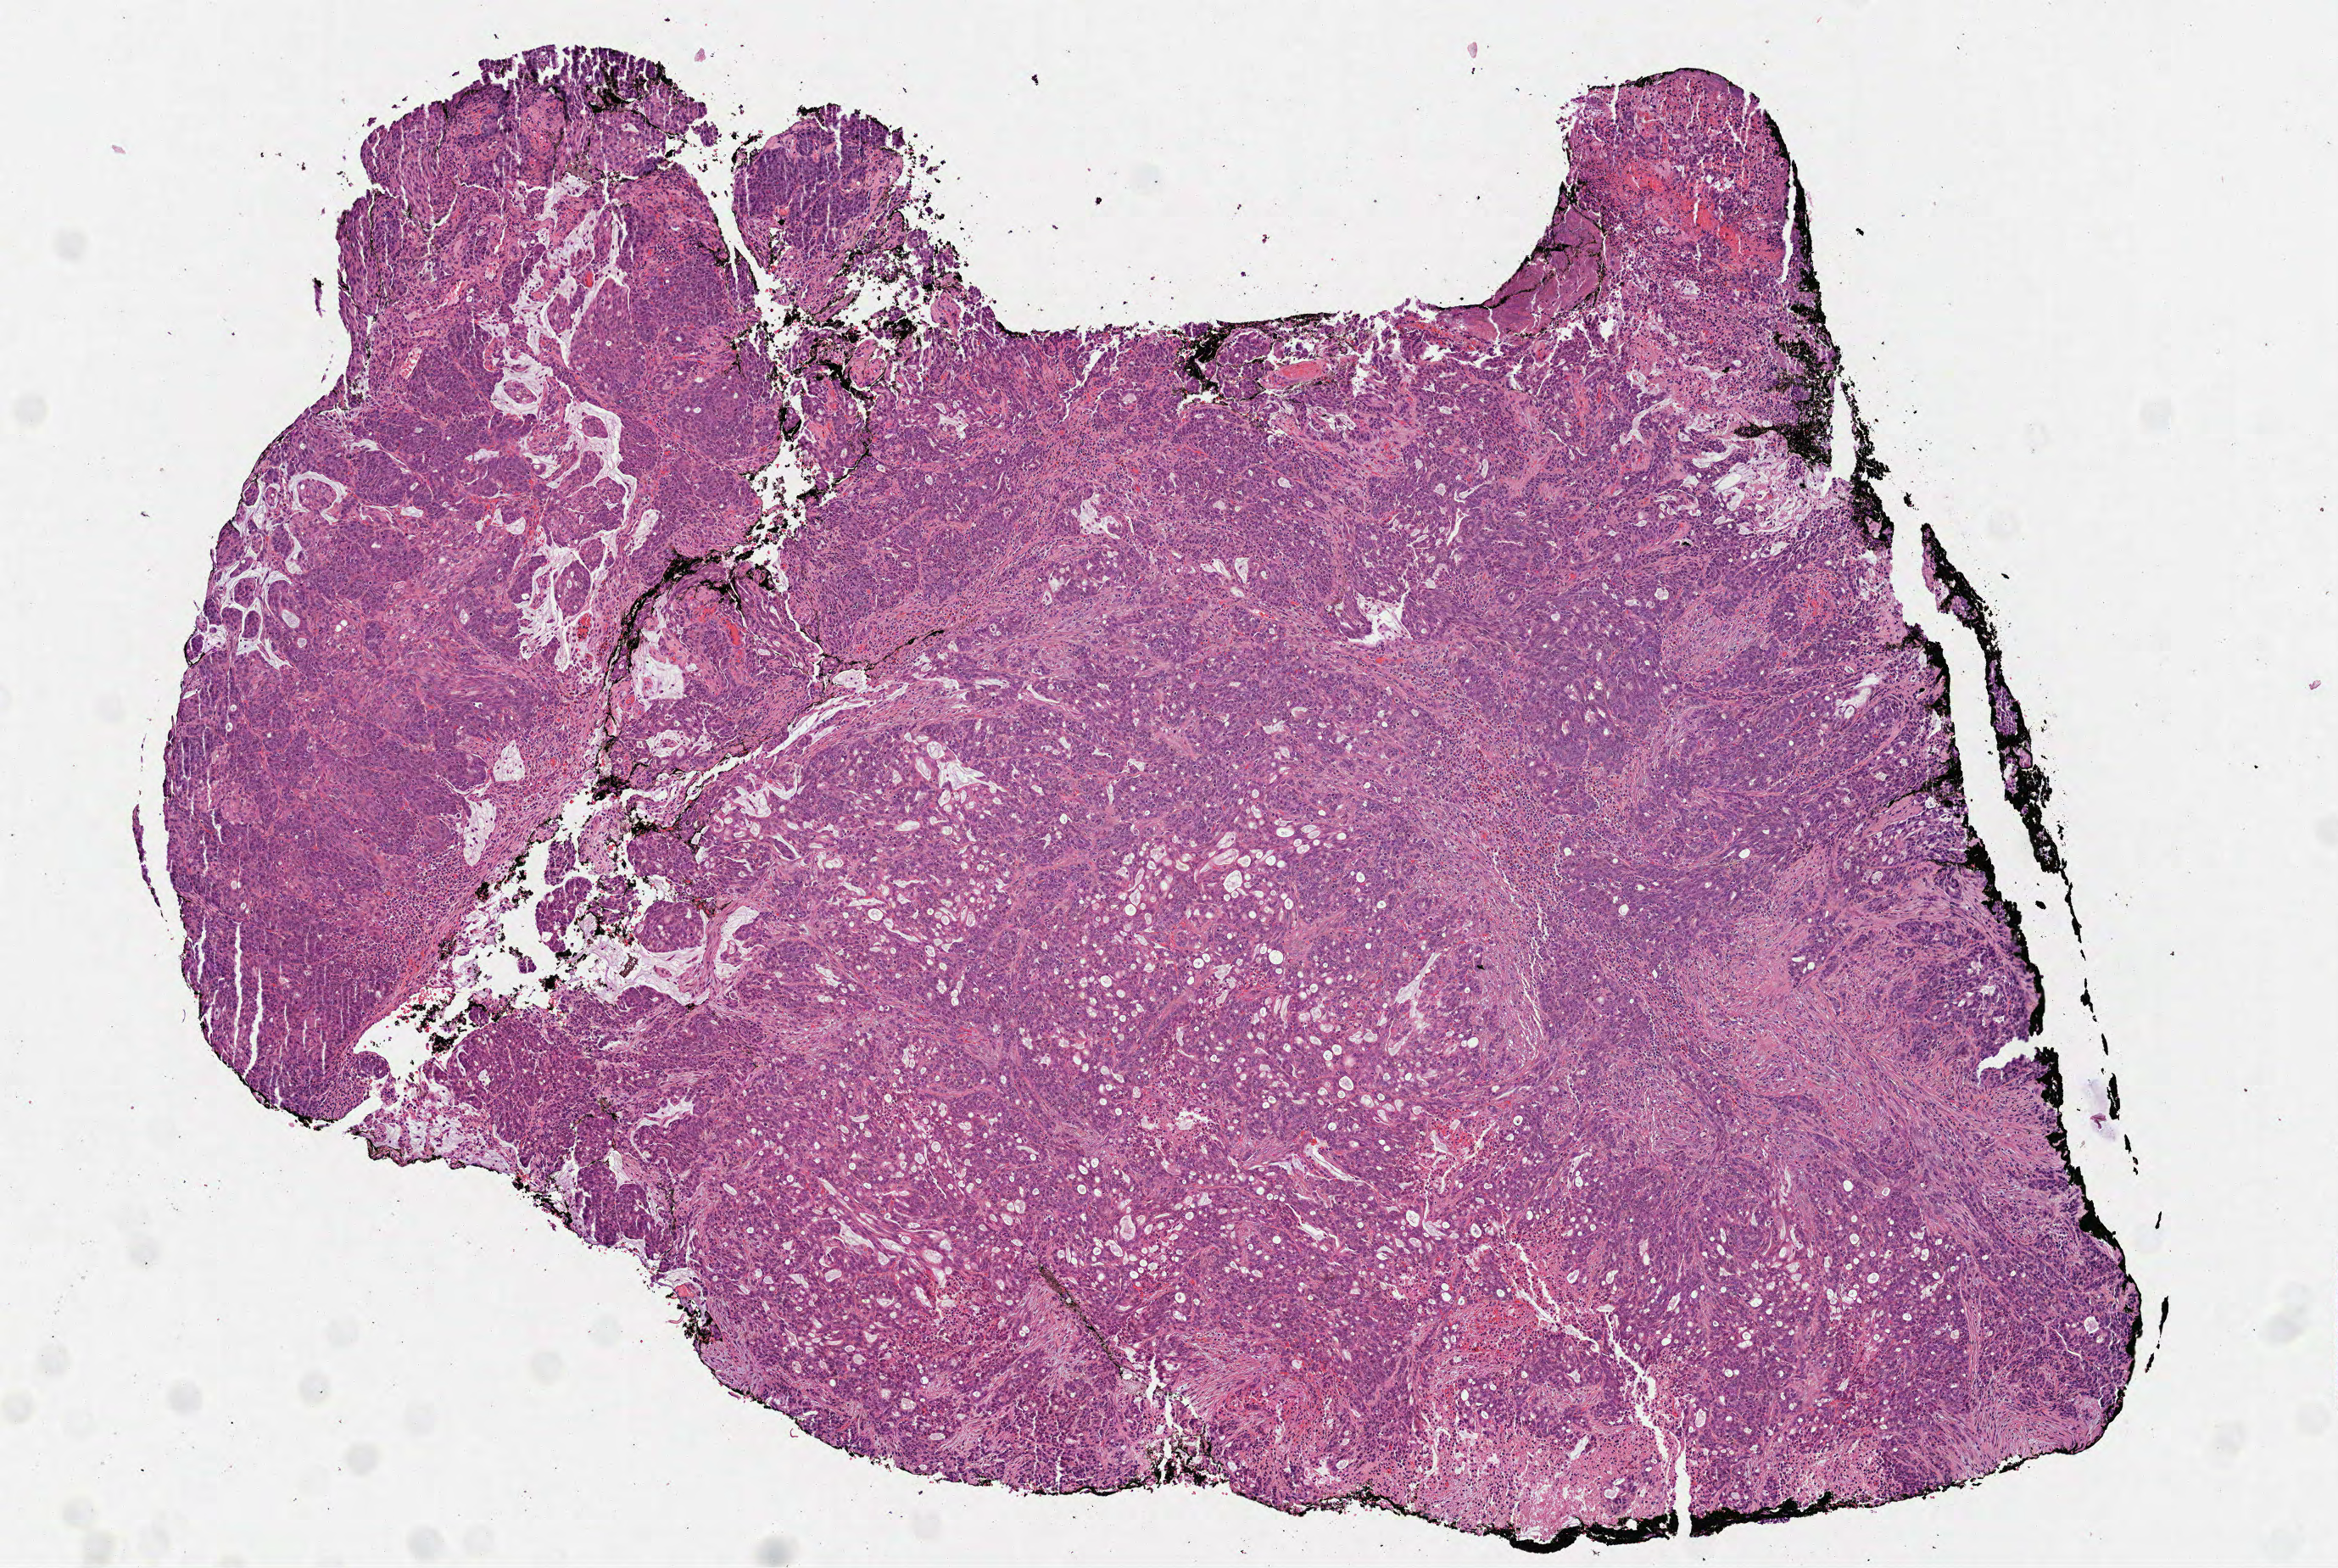
Digitized H&E-stained tissue section (whole slide), shown as a low-resolution overview of the whole scanned area (about 5.6 x 3.7 mm). Formalin-fixed paraffin-embedded (FFPE) diagnostic section. Sample: primary tumour, colon. Patient: male, age at initial diagnosis 84 years.
AJCC pathologic stage: IIIB (7th edition). Lymph nodes positive (case pathology): 1 of 17 examined. Histologic diagnosis: Adenocarcinoma, NOS (cecum). TNM: T3 N1a M0.